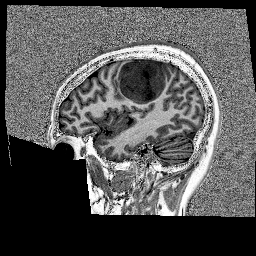
Brain MRI from a brain-tumour surgery series, one sagittal slice; position 49 of 176 along the scan axis; 1 mm slice thickness; 256 × 256 image matrix, field of view 256 × 256 mm. Case-level facts recorded for this patient, not image findings: histopathology: Glioblastoma; WHO grade: 4; IDH mutation: no; tumour location: Left Frontal.
Structures marked on this image (expert manual segmentation):
- tumour: bounding box <118,58,175,105> (left, top, right, bottom; pixels)